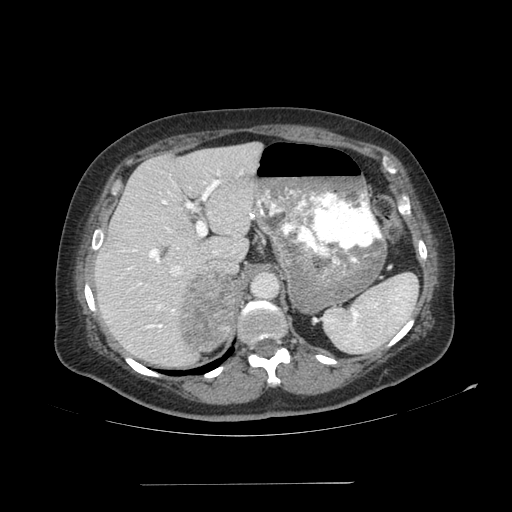
Contrast-enhanced abdominal CT, one axial slice; slice 73 of 113 in the series (ordered by position); 120 kVp; soft-tissue window (W 400 / L 40 HU); 512 × 512 image matrix, field of view 440 × 440 mm. Patient: female, 67 years. From the clinical record (not read from this slice): diagnosis: adrenocortical carcinoma; tumour side: right adrenal.
Outlined on this slice (semi-automatic segmentation, software-assisted and operator-edited):
- mass: bounding box (x1, y1, x2, y2) in pixels: (181, 275, 240, 352)